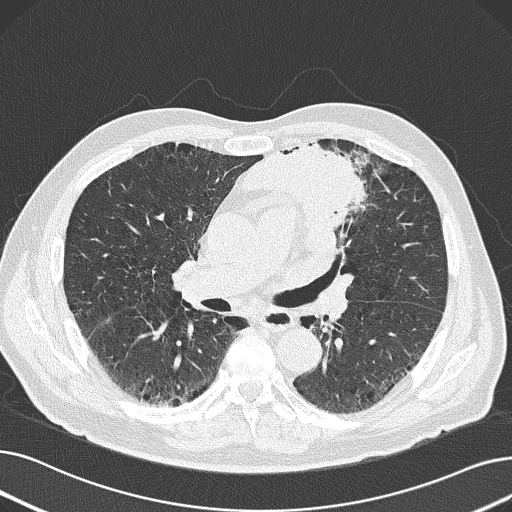
Low-dose screening chest CT, axial slice; baseline screening round; lung window (W 1500 / L -600 HU); 2 mm slice thickness; lung (sharp) reconstruction kernel (B50f); 120 kVp; slice 80 of 165 in the series; 512 × 512 image matrix, field of view 370 × 370 mm. Male, age 69 years at enrolment. Former smoker at enrolment.
Expert reader's lesion annotation, bounding box [x1, y1, x2, y2] px = [238, 129, 386, 248]. Reader record for this screening exam (exam-level; its link to the box is not recorded): non-calcified nodule or mass ≥4 mm, left upper lobe, 6 × 10 mm, spiculated (stellate) margins, soft tissue attenuation. Participant outcome: lung cancer diagnosed 20 days after this screen — non-small cell carcinoma, left upper lobe, poorly differentiated (G3), stage IB (AJCC 6th edition), 100 mm at pathology.